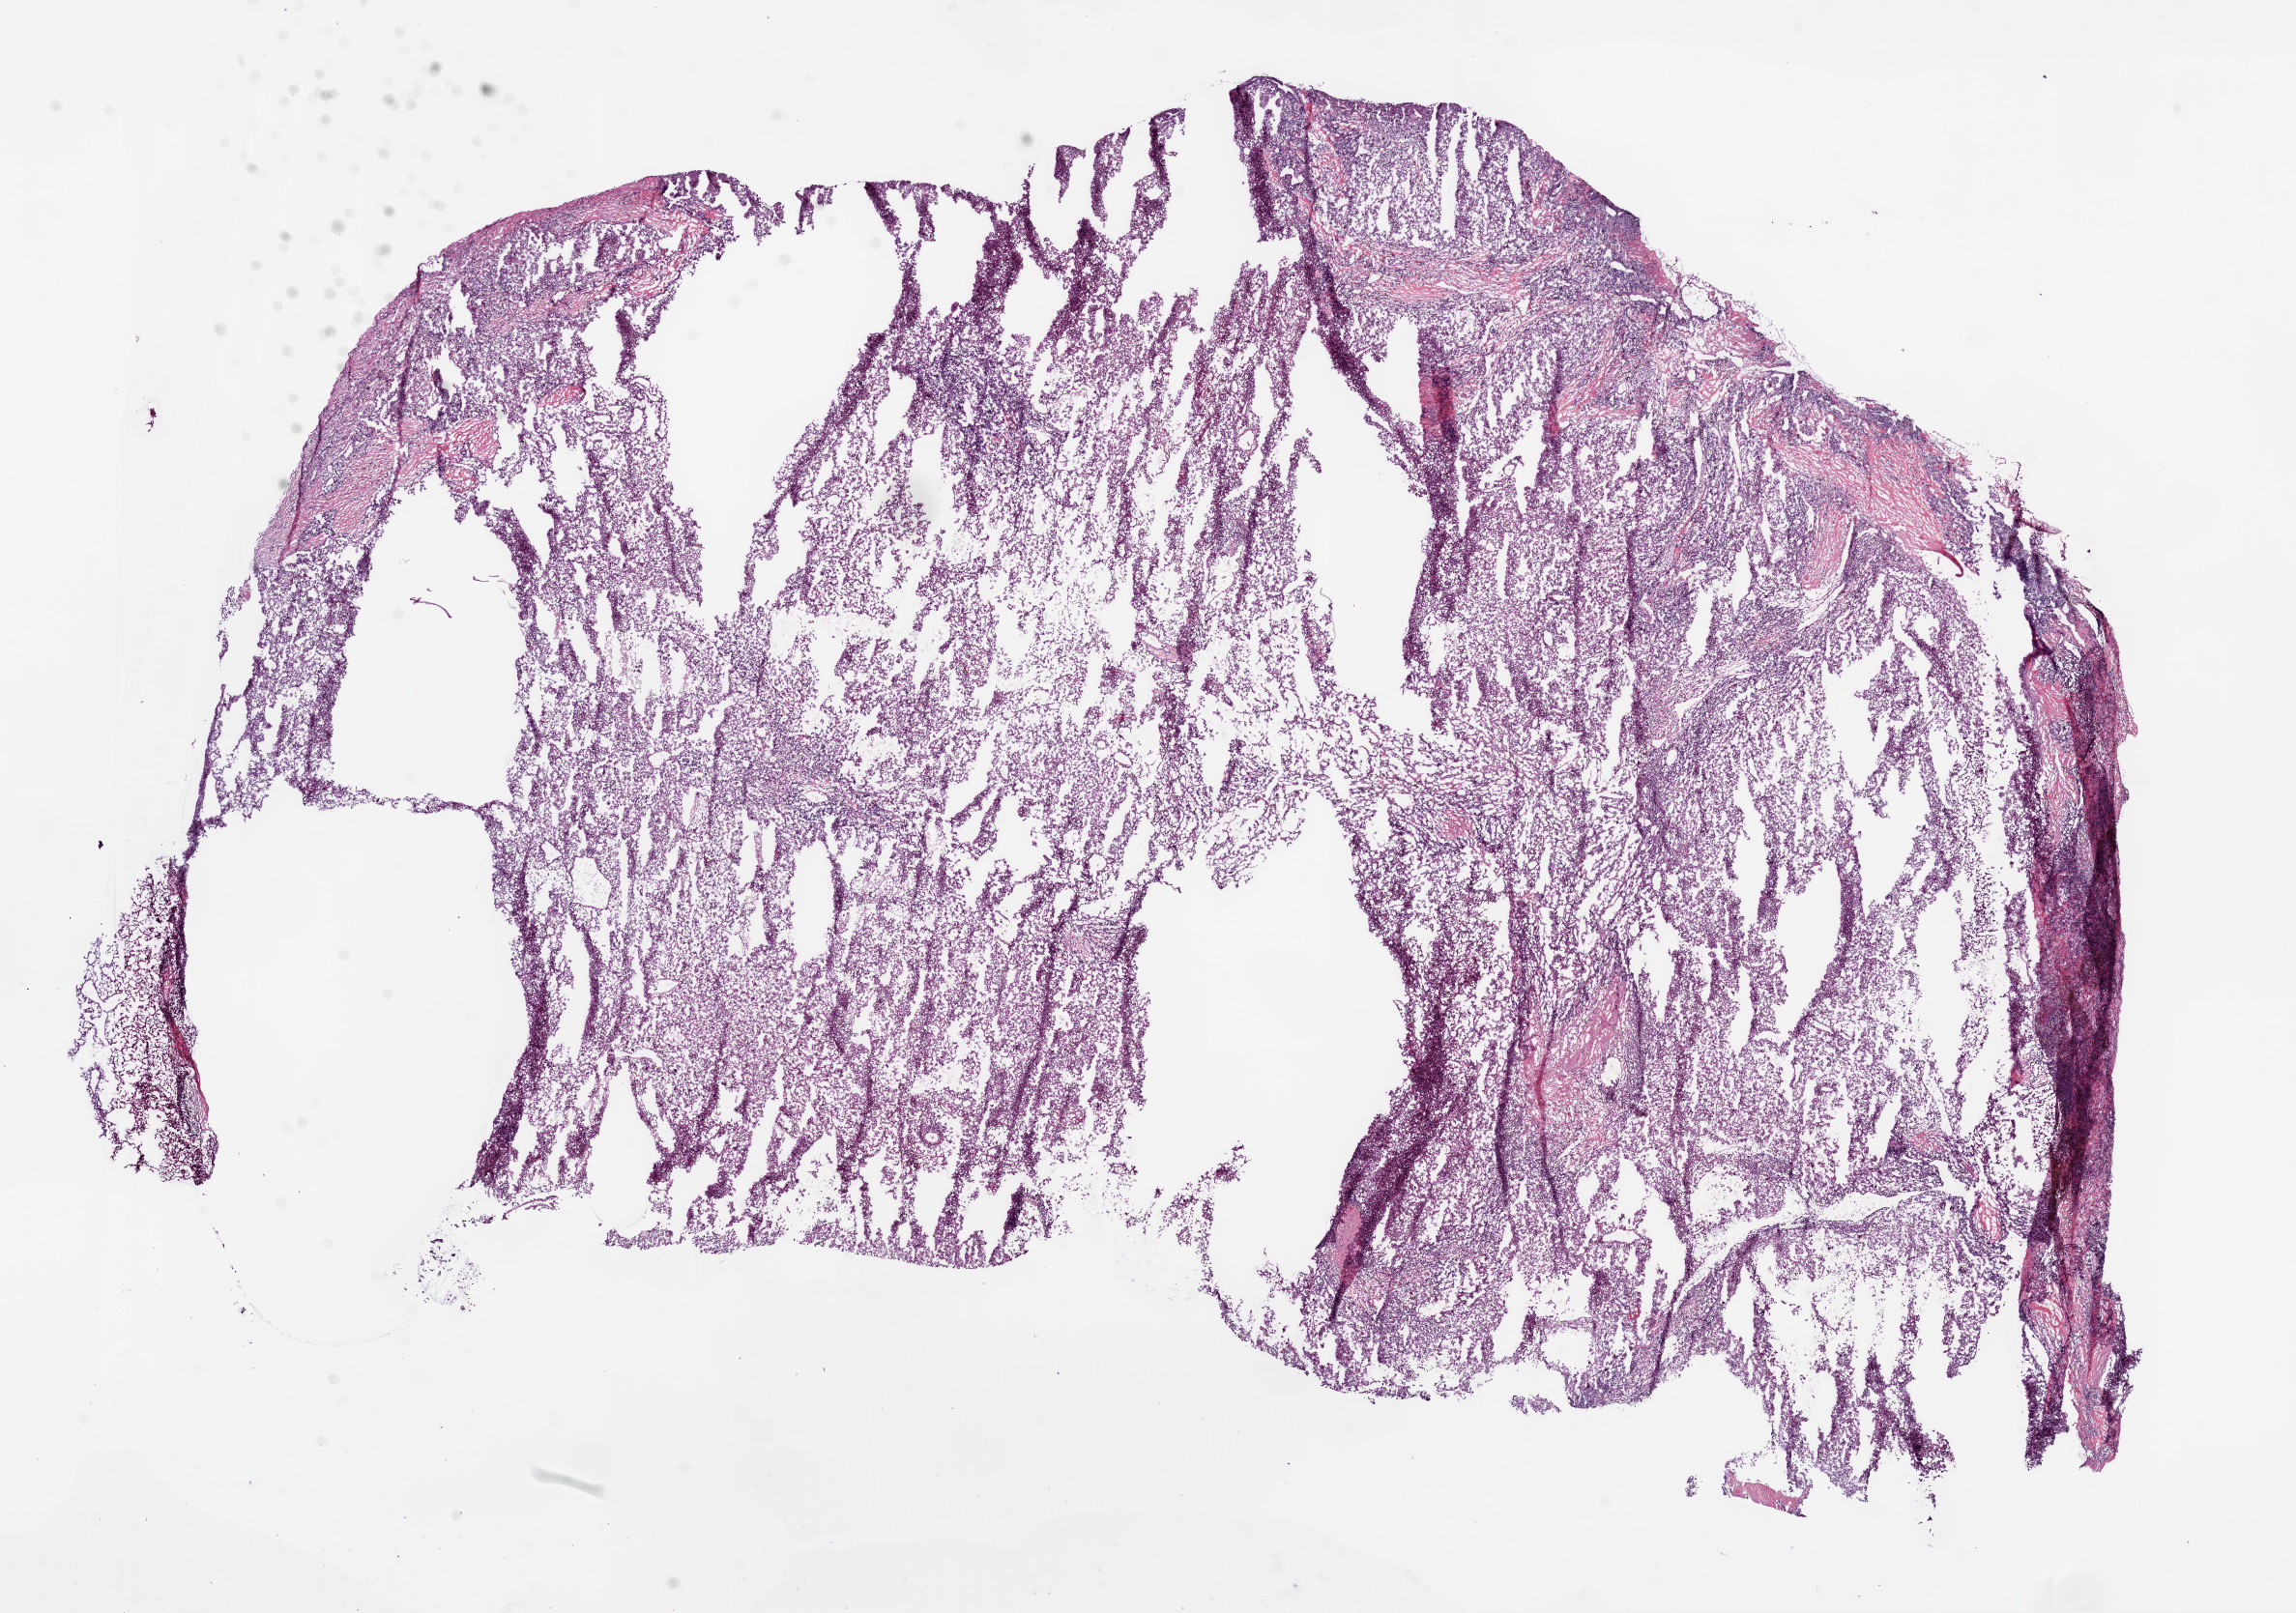
Digitized H&E-stained tissue section (whole slide), whole scanned area (about 19.1 x 13.4 mm) shown as a low-resolution overview, frozen section from the bottom of the tissue portion, primary tumour sample from the kidney. Patient: male, age at initial diagnosis 70 years. Histologic grade: G4 (undifferentiated). Slide review estimates, as recorded: tumour cells 90%, tumour nuclei 80%, normal cells 0%, stromal cells 10%, necrosis 0%.
• lymph nodes positive (case pathology): 0 of 9 examined
• AJCC pathologic stage: I
• TNM: T1b N0 M0
• histologic diagnosis: Clear cell adenocarcinoma, NOS